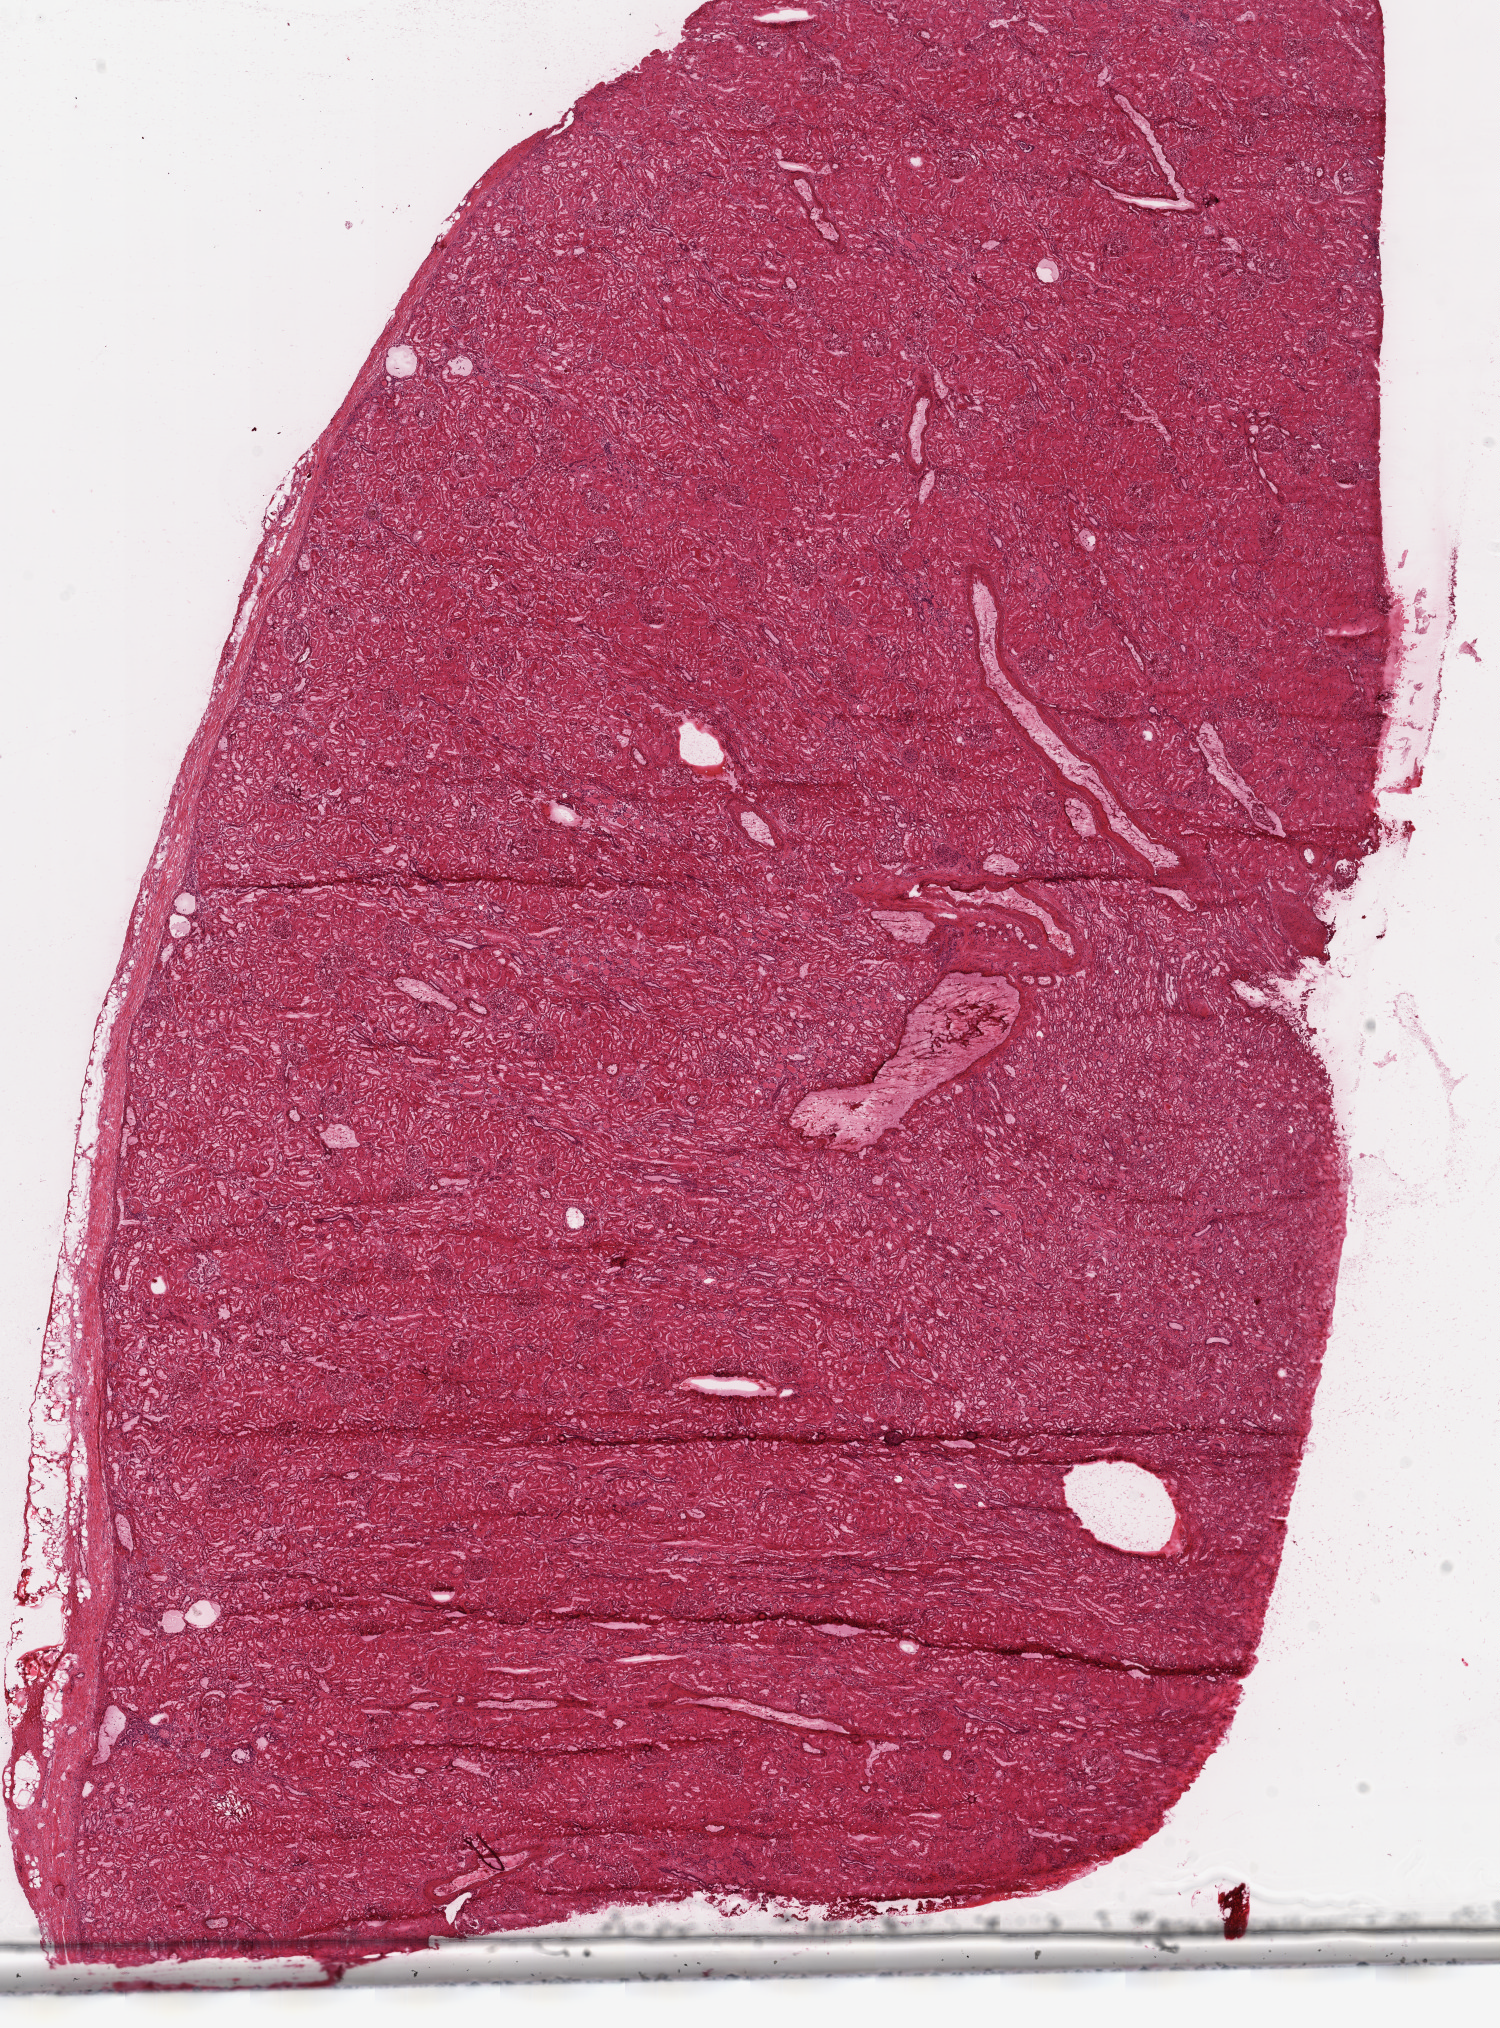
H&E whole-slide image — whole scanned area (about 12.0 x 16.3 mm, acquisition: 20x scan) shown as a low-resolution overview; frozen section from the top of the tissue portion; sample: solid tissue normal (non-tumour tissue), kidney. Female patient; age at initial diagnosis 46 years.
- this section: solid tissue normal (non-tumour) sample from the same patient
- patient diagnosis: Clear cell adenocarcinoma, NOS